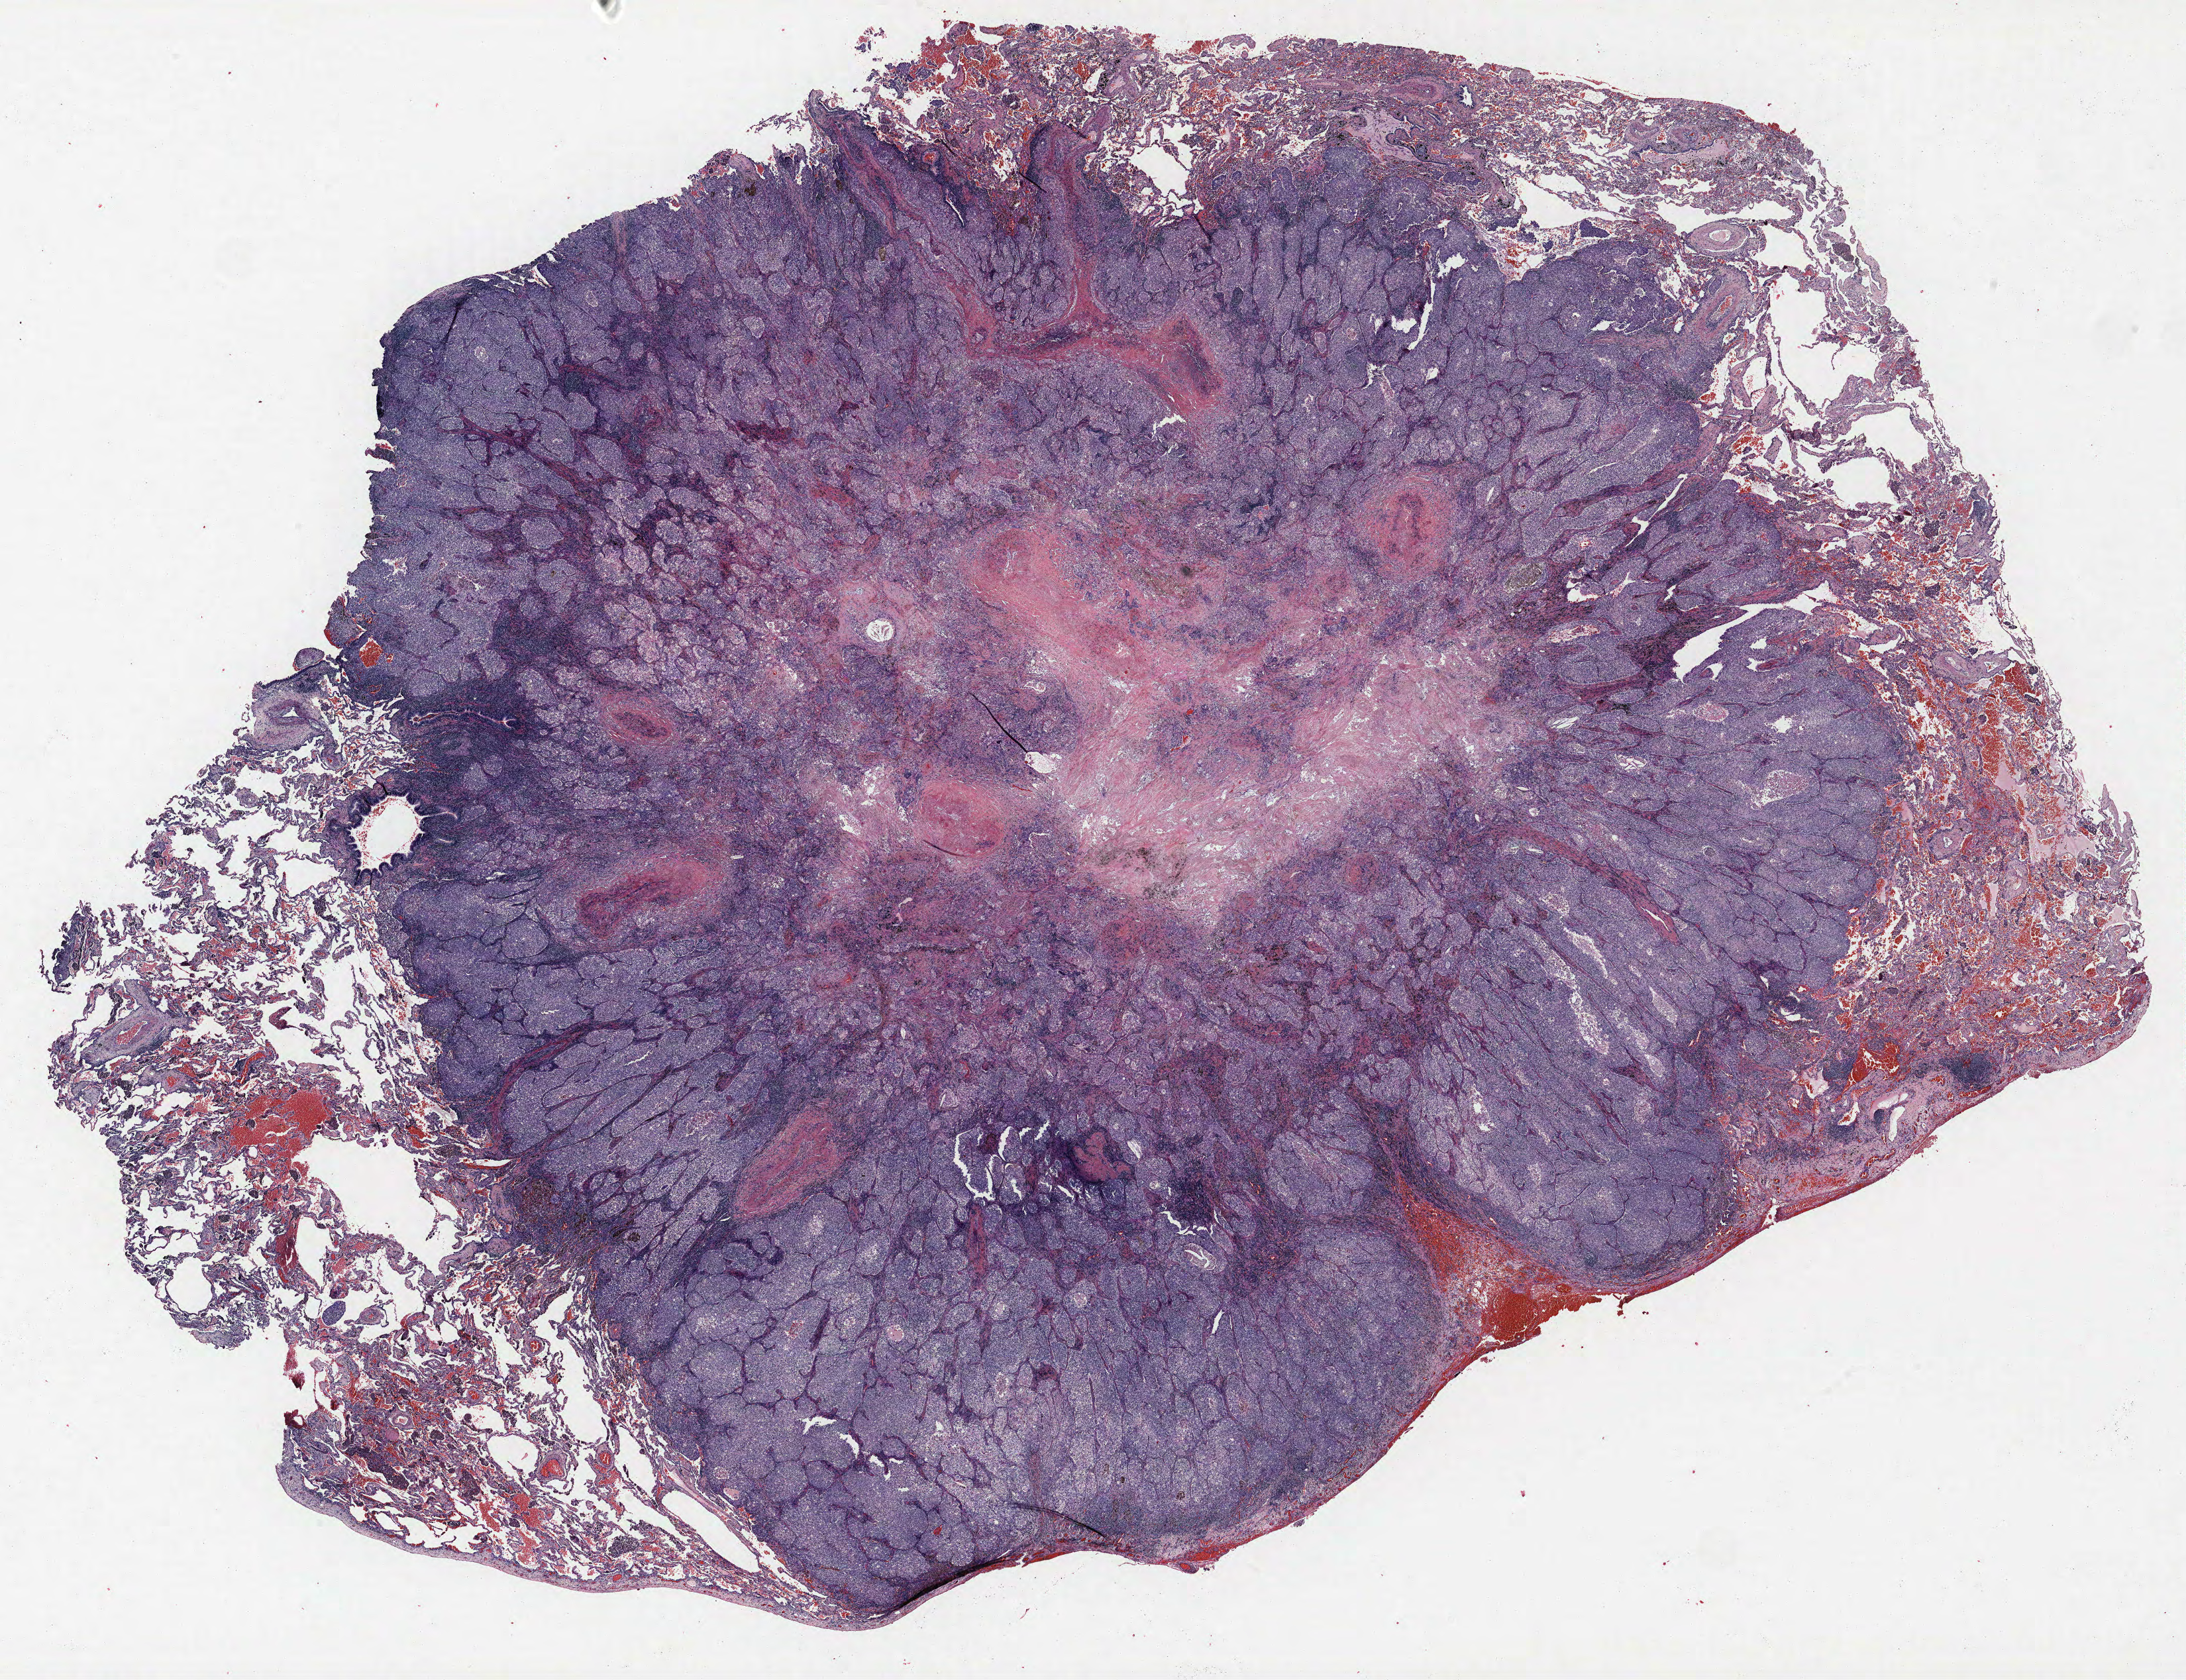
Whole-slide histology image, Hematoxylin and eosin (H&E) stained — a low-resolution overview of the entire scanned area, about 26.4 x 20.3 mm (acquisition: 40x scan), FFPE section, lung tissue. Female, age 56 at enrolment. Grade: poorly differentiated (G3).
Primary tumour location (clinical record): right upper lobe. Stage (AJCC 6th edition): IIA. Tumour size (pathology): 20 mm. Participant's lung-cancer diagnosis: Adenocarcinoma, NOS.